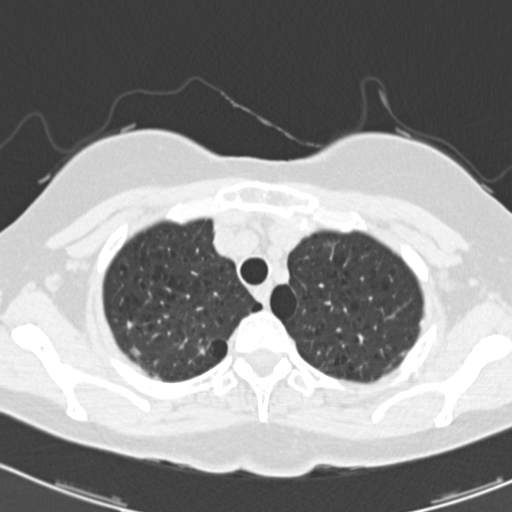
Chest CT (low-dose screening protocol), one axial image. First (baseline) screen. Lung window (W 1500 / L -600 HU). Standard (soft-tissue) reconstruction kernel (B30f). 120 kVp. Female participant, aged 64 years at enrolment.
Expert-annotated lung lesion, bounding box [x1, y1, x2, y2] px = [181, 333, 230, 366]. No non-calcified nodule or mass ≥4 mm was recorded by the screening reader at this exam. Official screen result: negative screen, minor abnormalities not suspicious for lung cancer.